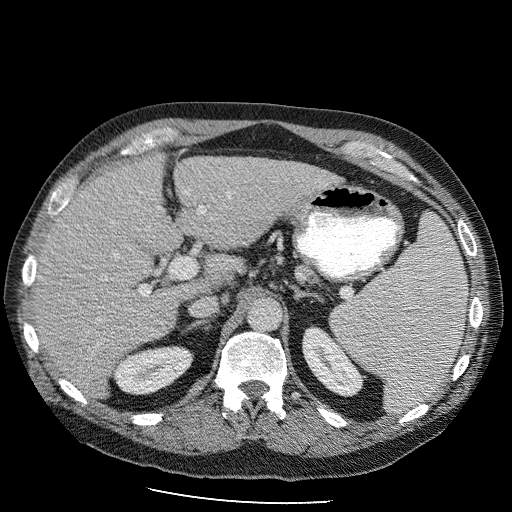
Contrast-enhanced abdominal CT (liver protocol), one axial slice. Position 60 of 98 along the scan axis. Soft-tissue window (W 400 / L 40 HU). 512 × 512 image matrix, field of view 400 × 400 mm. From the clinical record (not read from this slice): diagnosis: hepatocellular carcinoma (patient treated with transarterial chemoembolisation; whether this scan precedes or follows treatment is not stated here); TNM stage (as recorded): Stage-II; Child-Pugh class: B; tumour nodularity: uninodular.
Annotated regions visible in this slice (semi-automatically segmented with operator editing):
- liver parenchyma outside the tumour (the mass and vessels are separate outlines, so this box may not span the whole liver): bounding box [x1, y1, x2, y2] px = [36, 148, 352, 397]
- liver vessels: [93, 201, 209, 336]